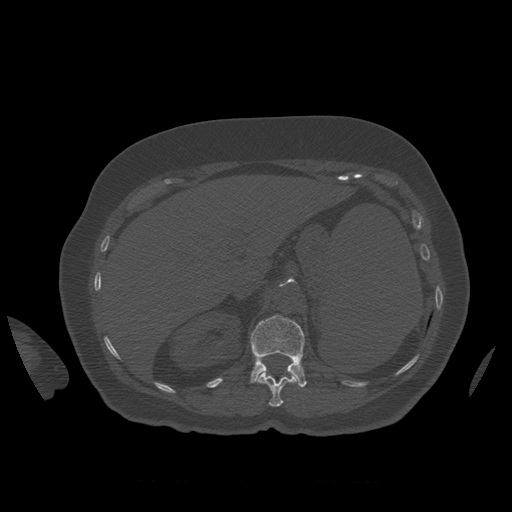
CT including the spine, one axial slice; slice 288 of 399 in the series (ordered by position); reconstruction kernel STANDARD; bone window (W 1800 / L 400 HU); 512 × 512 image matrix. Patient age 81 years. From the clinical record (not read from this slice): primary cancer: renal.
Annotated regions visible in this slice (semi-automatic segmentation, software-assisted and operator-edited):
- L1 vertebra: bounding box (x1, y1, x2, y2) in pixels: (250, 315, 307, 388)
- T12 vertebra: (257, 372, 297, 407)